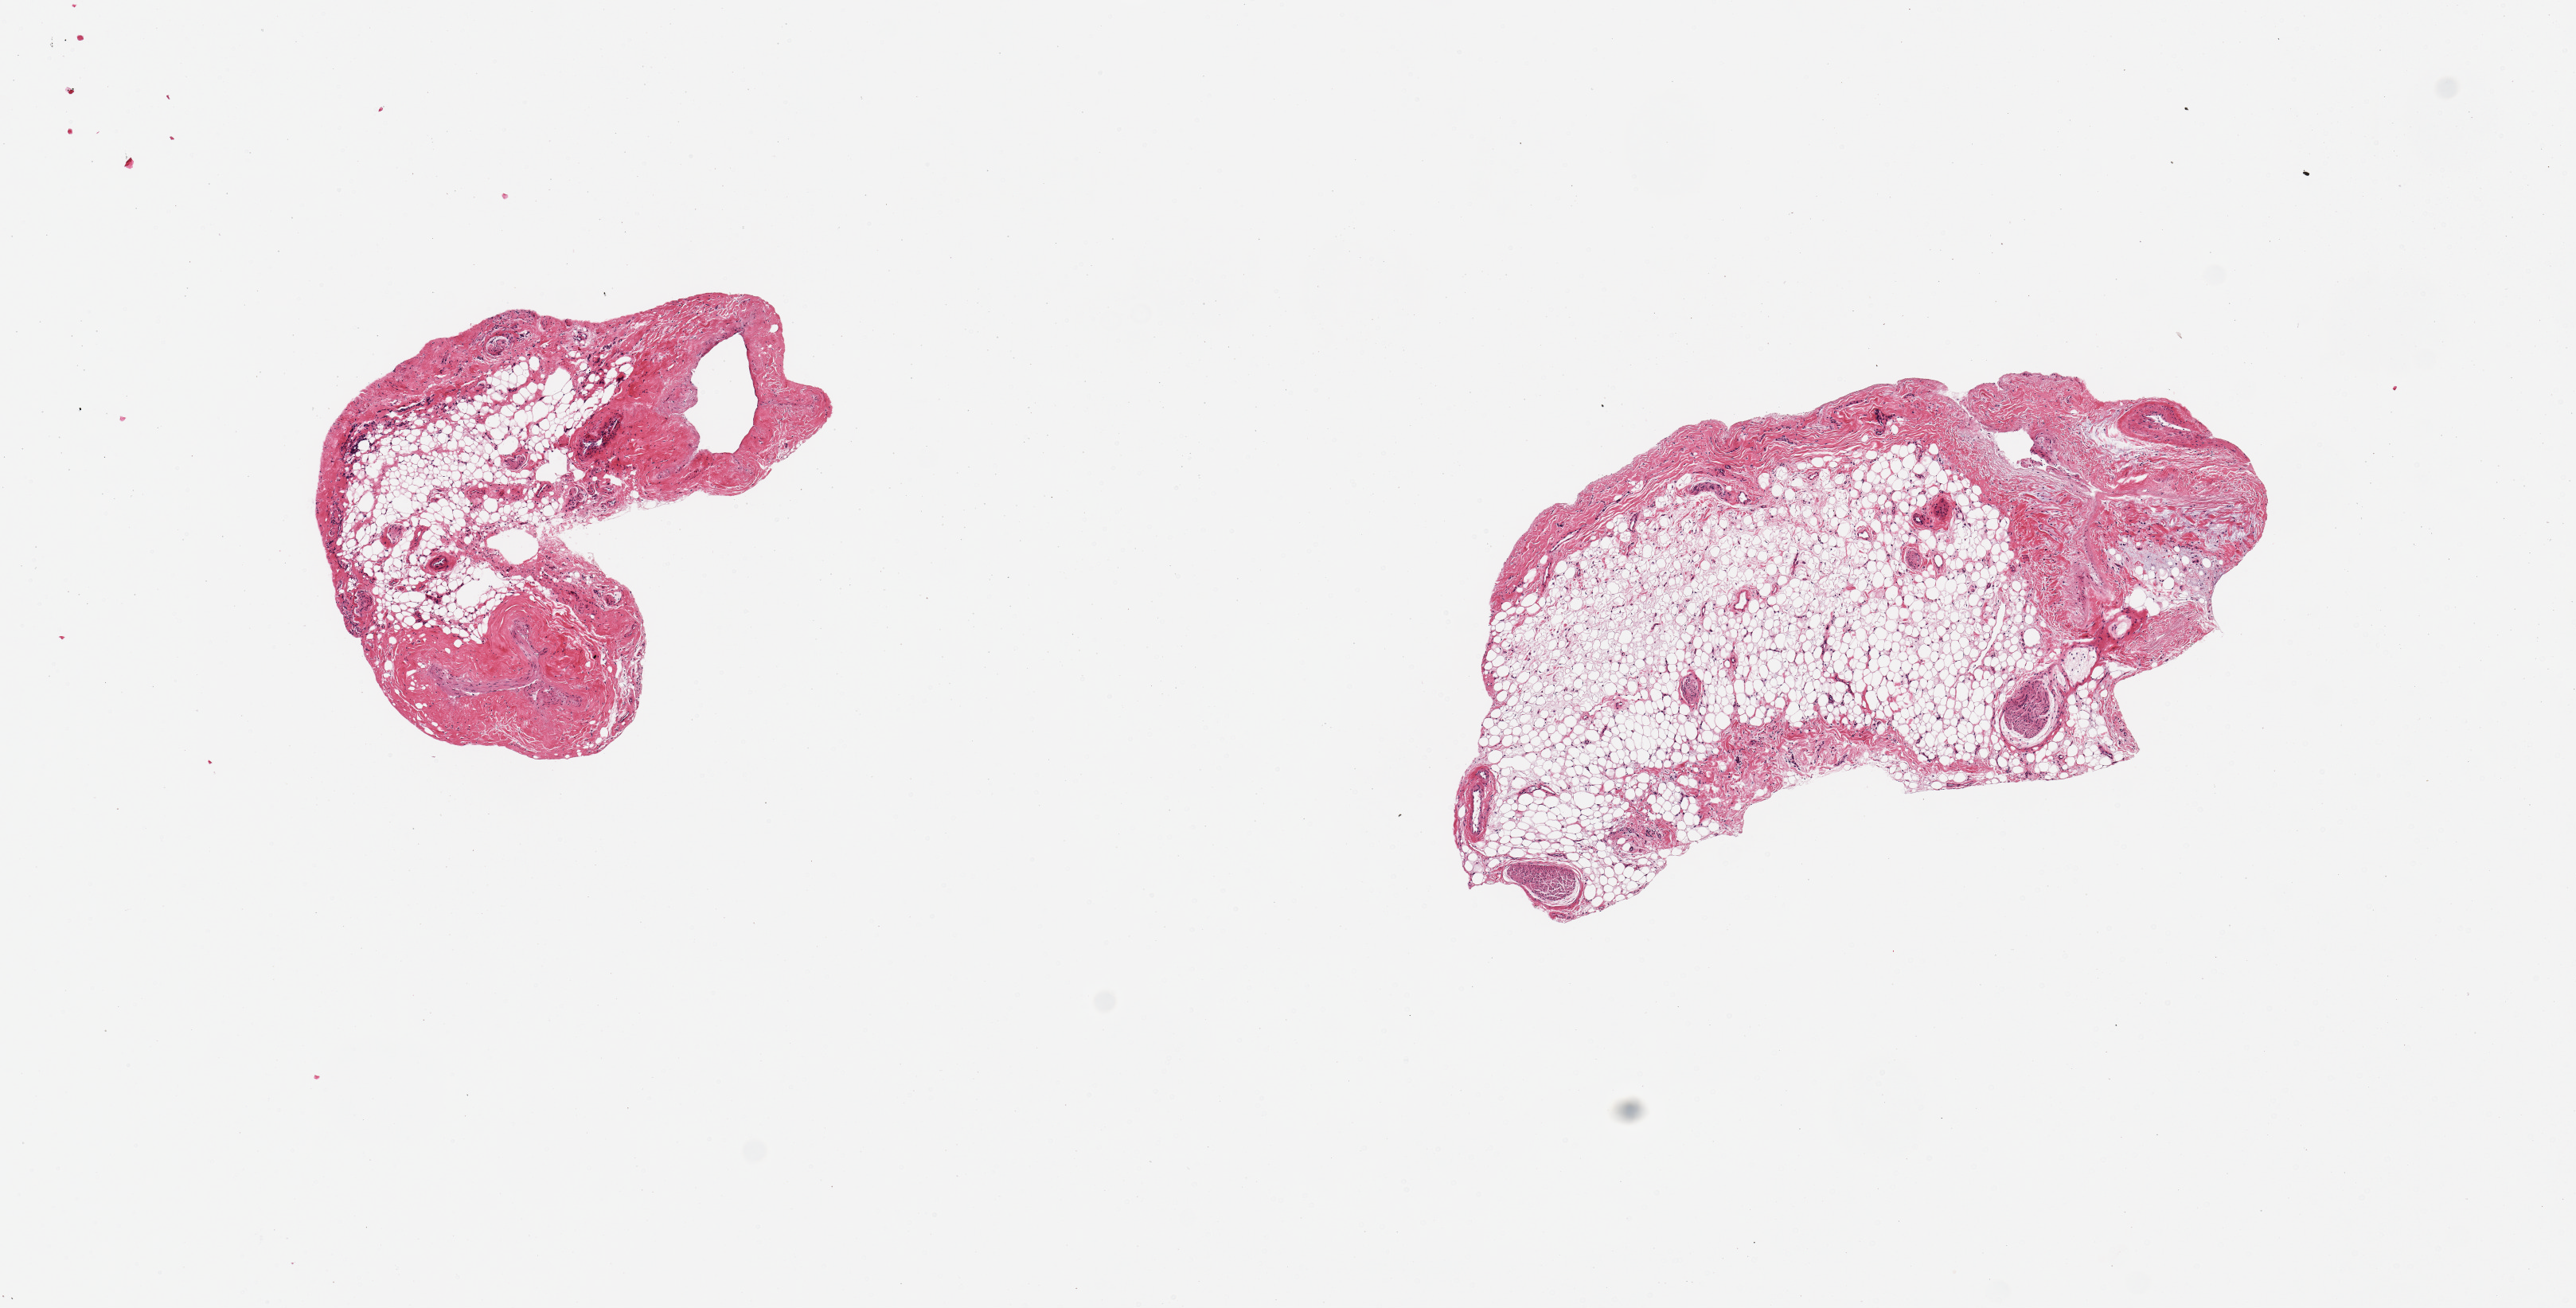
Whole-slide image, H&E stain, brightfield, shown as a low-resolution overview of the whole scanned area (about 12.8 x 6.5 mm); PAXgene-fixed paraffin-embedded (PFPE) section; sampled site (target tissue): coronary artery; tissue donor sample. Donor sex: female.
Review note (as recorded): Epicardial fat and myometrium no coronary artery present.